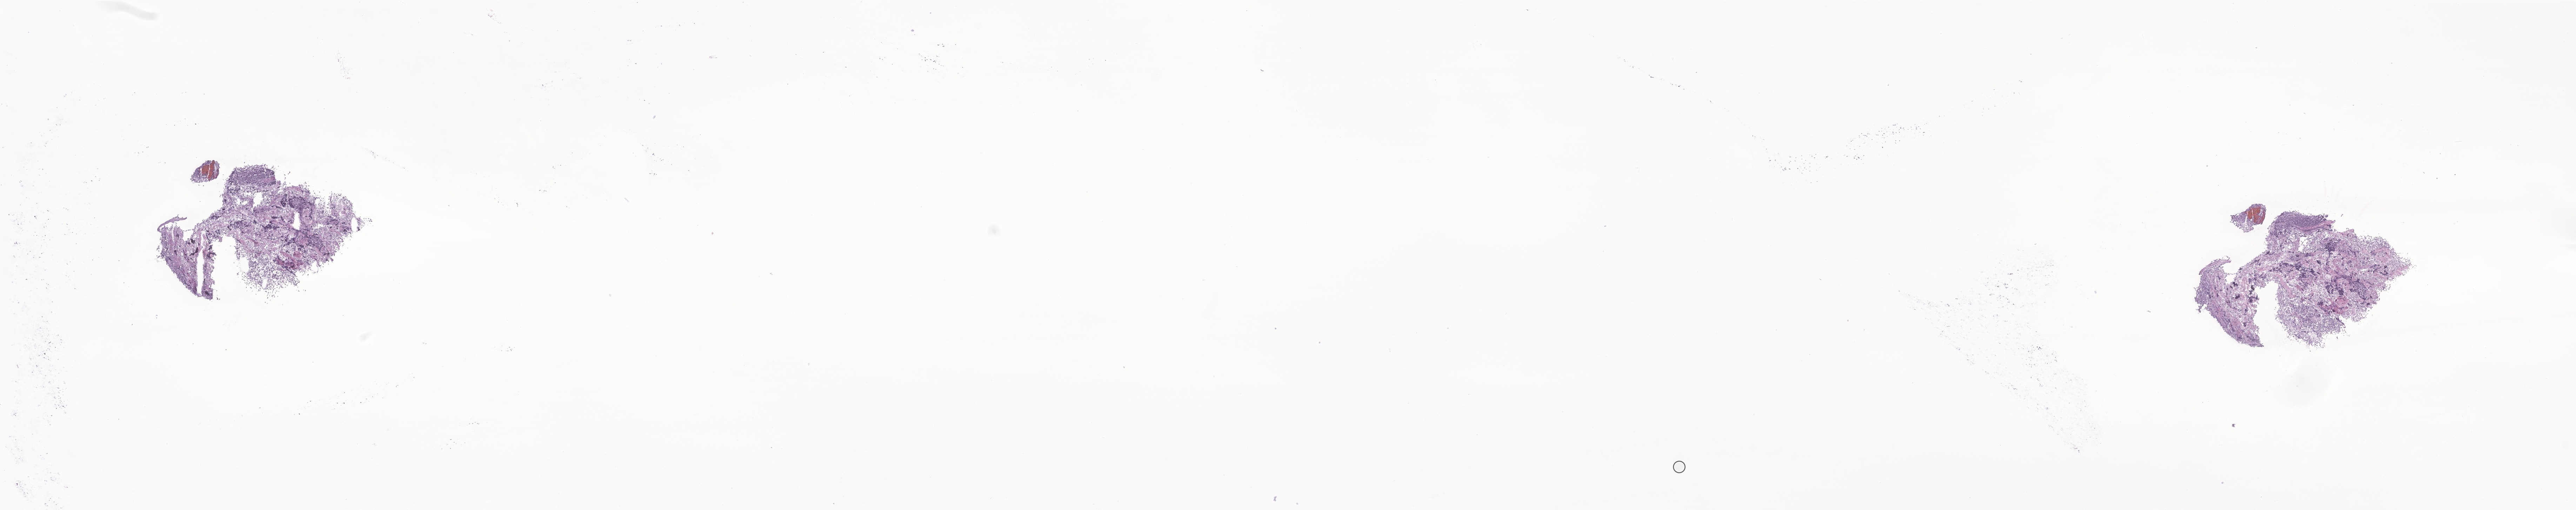
Haematoxylin and eosin whole-slide image of tumor tissue from the brain — shown as a low-resolution overview of the whole scanned area (about 31.0 x 6.1 mm); frozen section. Patient: male, age 197 months (16 years 5 months).
Recorded diagnosis: Medulloblastoma, NOS.